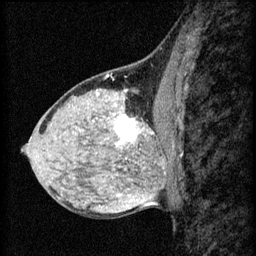
Breast MRI (dynamic contrast-enhanced), one sagittal slice. 3 images stored at this slice position (order not interpretable as contrast timing). 1.5 T. TE 4.2 ms, TR 8.2 ms. 256 × 256 image matrix, field of view 180 × 180 mm. Patient: female, 40 years.
Annotated regions visible in this slice (semi-automatic segmentation, software-assisted and operator-edited):
- analysis volume of interest (the breast-tissue region the enhancement analysis was run in; not a lesion): bounding box [x1, y1, x2, y2] px = [108, 108, 167, 159]
- tumour enhancement mask (voxels above the 70 % enhancement threshold inside the analysis volume of interest): [114, 116, 153, 145]